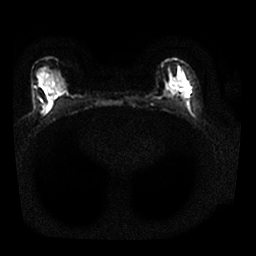
Breast MRI, one axial slice; slice 14 of 25 in the series (ordered by position); diffusion-weighted series; image 2 of 4 stored at this slice position (different b-values; order by instance number); 1.5 T; 256 × 256 image matrix, field of view 310 × 310 mm. Female patient.
Annotated regions visible in this slice (manually delineated by an expert):
- tumour on diffusion-weighted imaging: bounding box <185,93,189,96> (left, top, right, bottom; pixels)